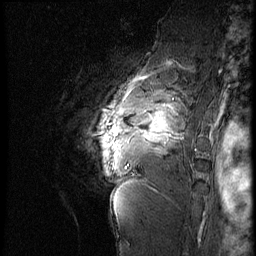
Breast MRI (dynamic contrast-enhanced), one sagittal slice. 4 images stored at this slice position (order not interpretable as contrast timing). 1.5 T. TE 4.2 ms, TR 9 ms. 2.5 mm slice thickness. 256 × 256 image matrix, field of view 180 × 180 mm. Female patient, age 56 years. Case-level facts recorded for this patient, not image findings: setting: breast cancer imaged before/during neoadjuvant chemotherapy; receptor status: HER2-positive.
Annotated regions visible in this slice (semi-automatic segmentation, software-assisted and operator-edited):
- analysis volume of interest (the breast-tissue region the enhancement analysis was run in; not a lesion): box from (x=82, y=83) to (x=199, y=177) px
- tumour enhancement mask (voxels above the 140 % enhancement threshold inside the analysis volume of interest): (x=113, y=105)–(x=175, y=144)